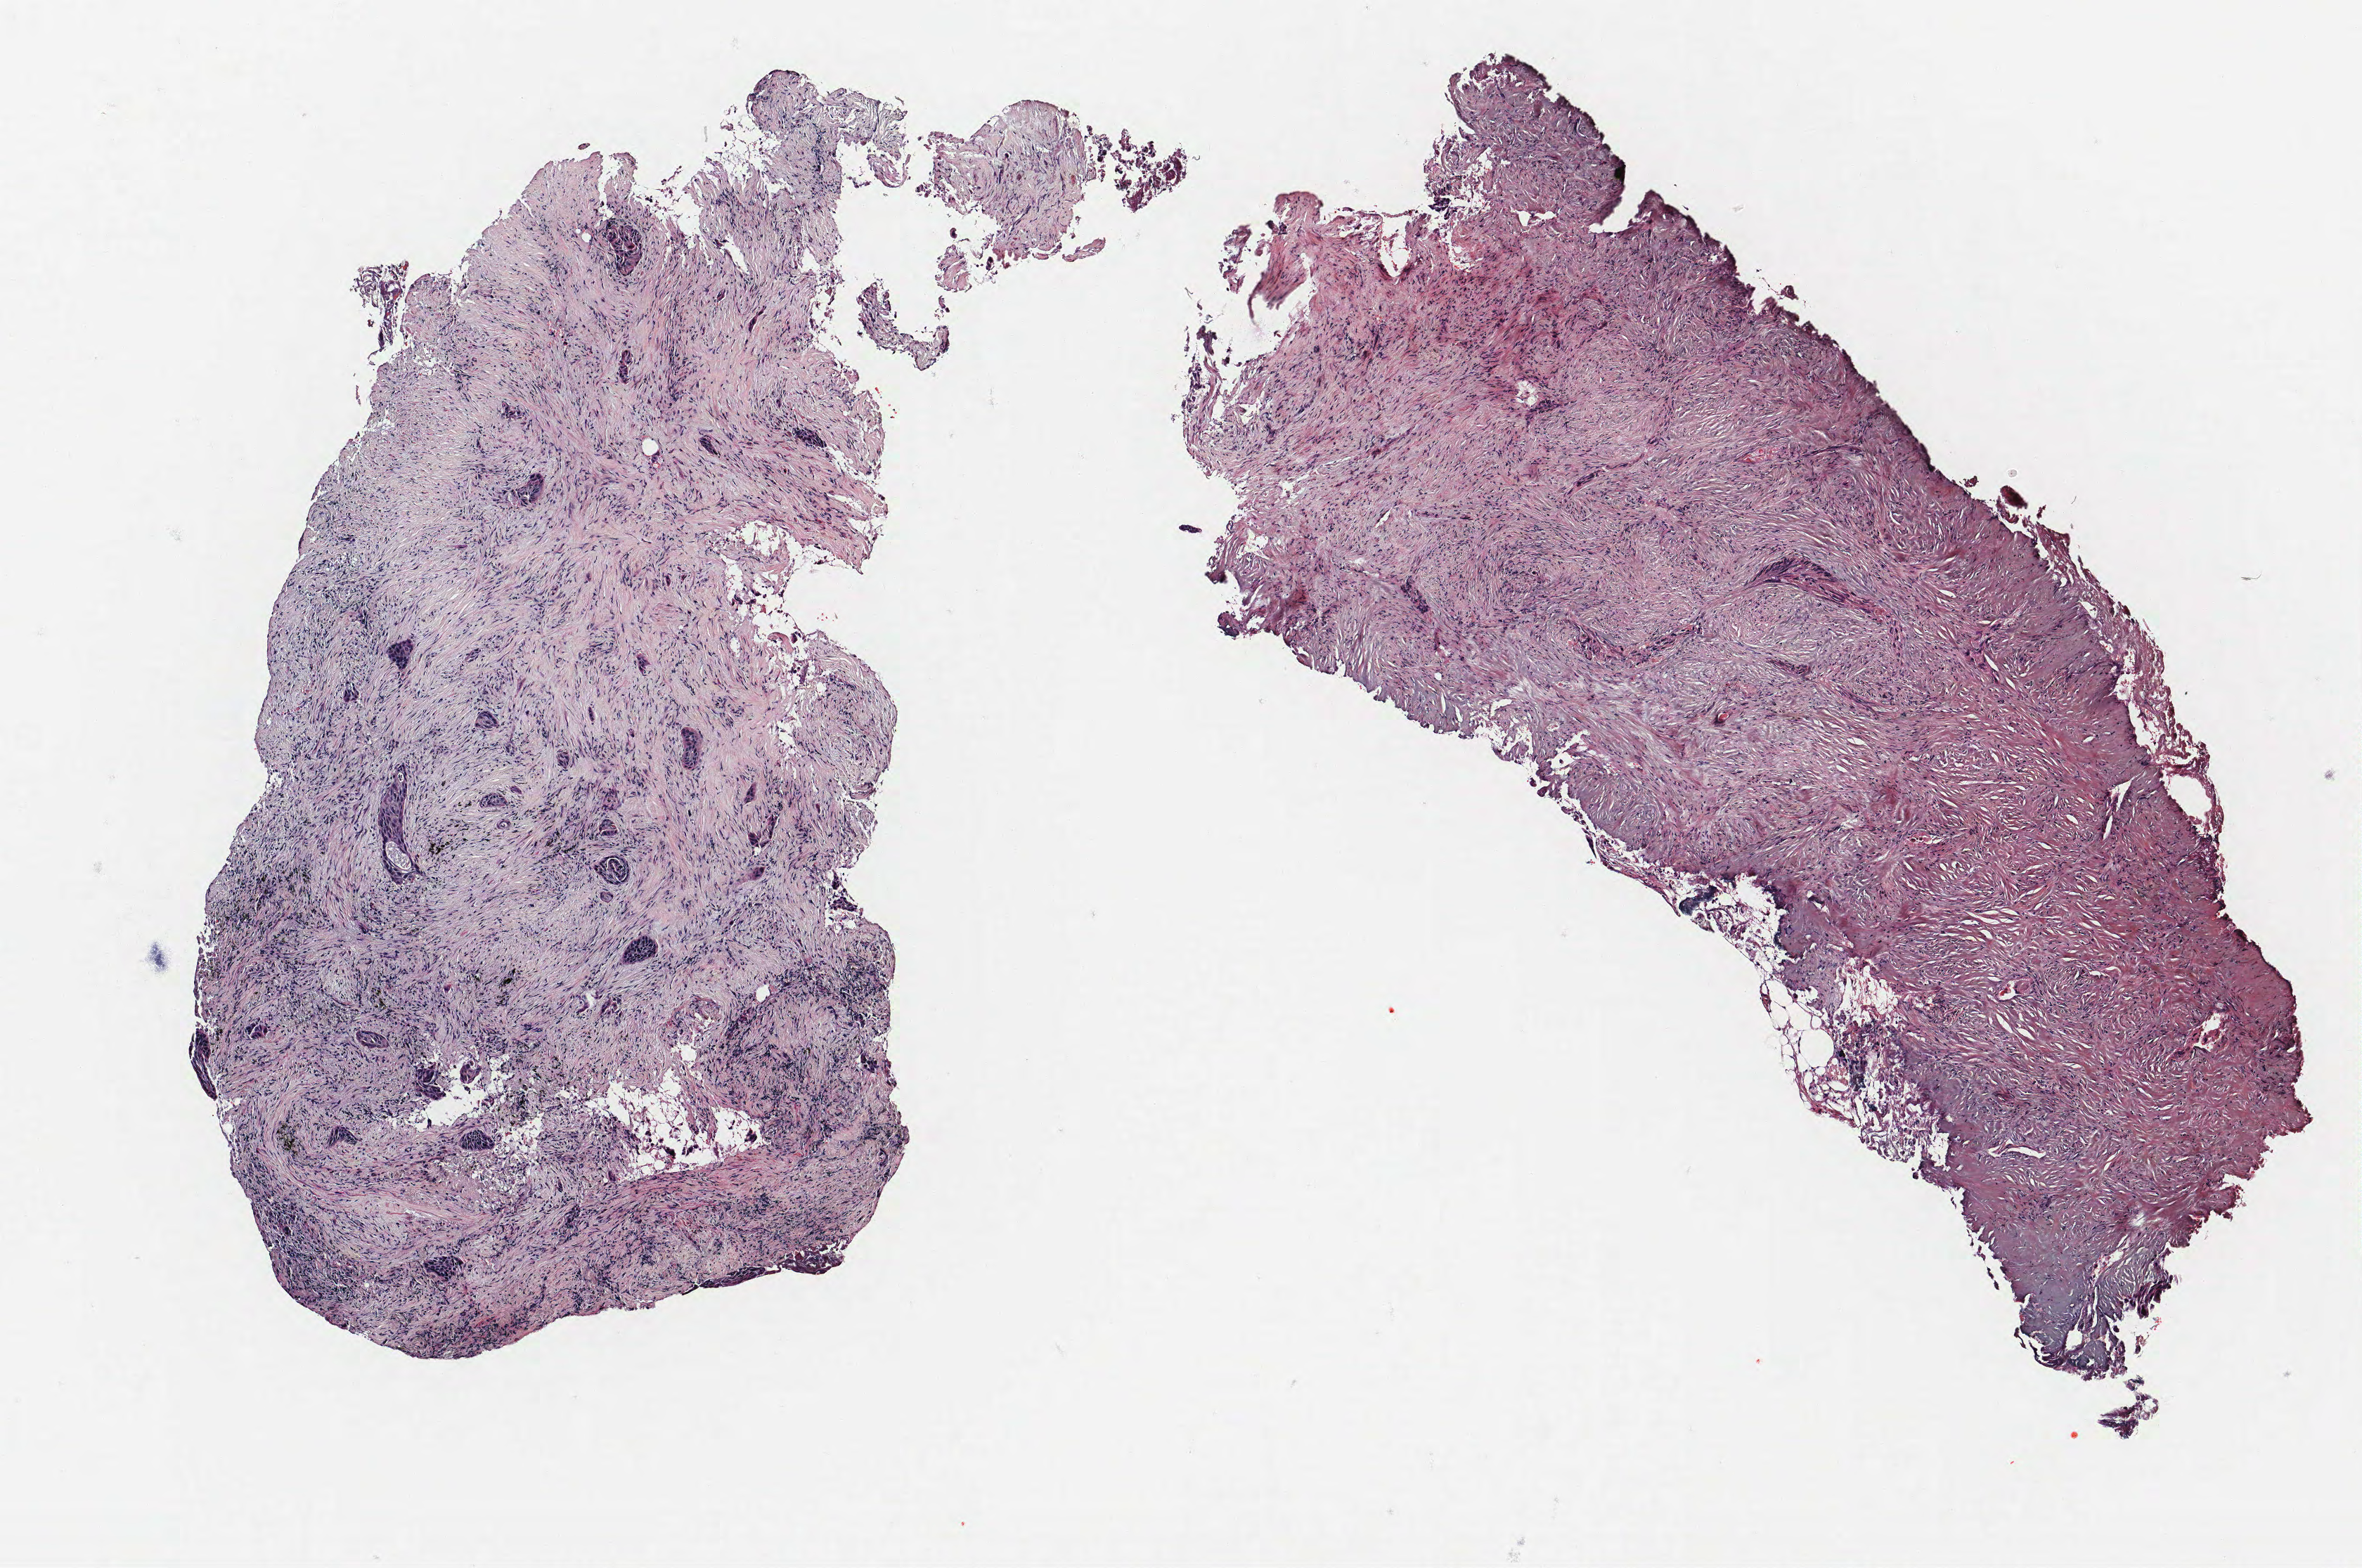
Hematoxylin and eosin (H&E) stained whole-slide image, shown as a low-resolution overview of the whole scanned area (about 6.7 x 4.5 mm, slide scanned at 40x). Formalin-fixed paraffin-embedded (FFPE) section. Lung. Male patient, aged 61 at enrolment. Former smoker at enrolment. Grade: moderately differentiated (G2).
• participant's lung-cancer diagnosis: Squamous cell carcinoma, NOS (ICD-O-3 8070/3)
• tumour size (pathology): 25 mm
• stage (AJCC 6th edition): IIIB
• ICD-O-3 topography: middle lobe of lung (C34.2)
• primary tumour location (clinical record): right middle lobe